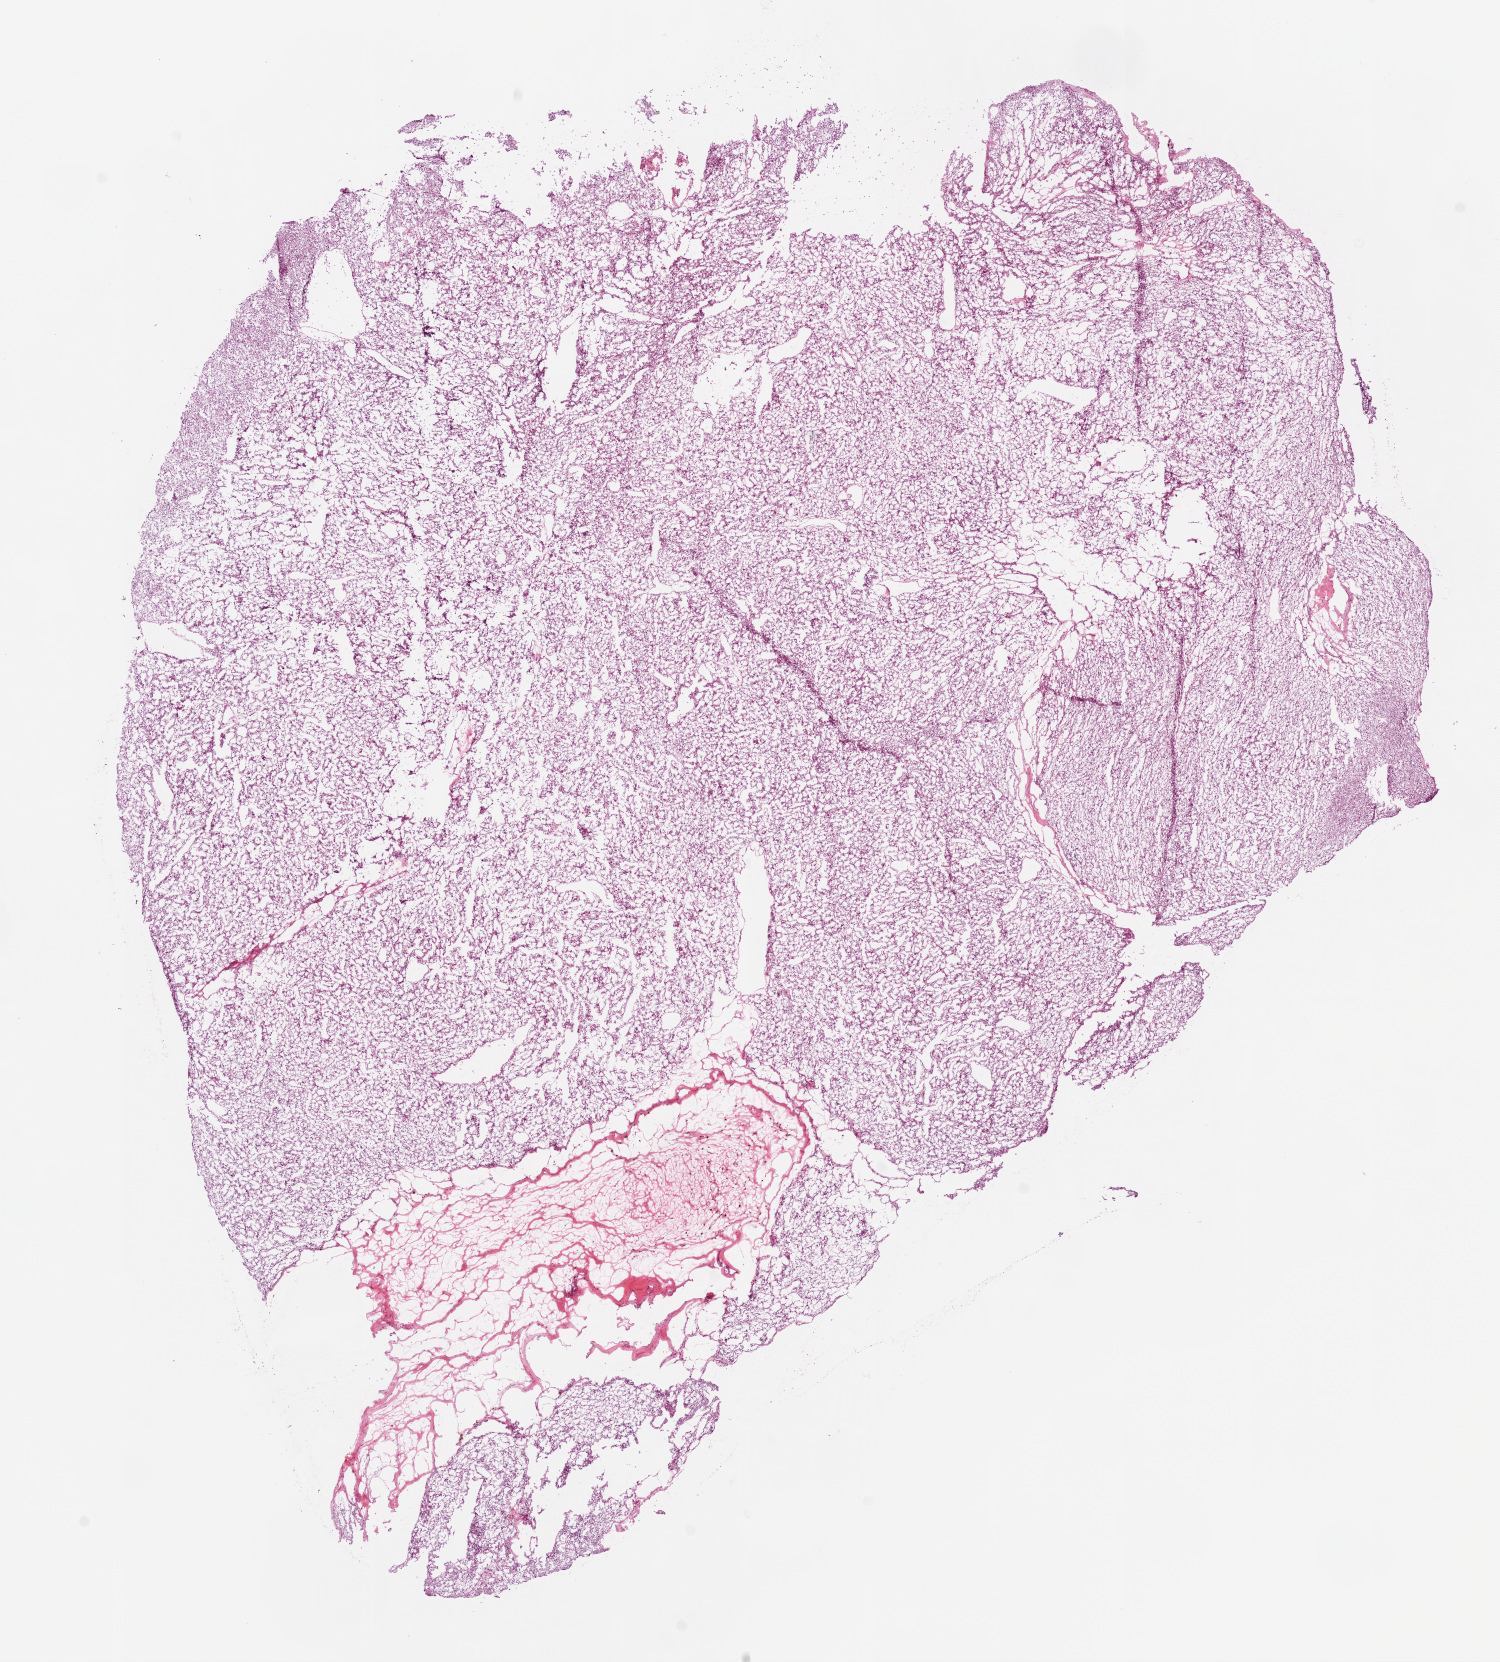
Whole-slide histology image, H&E, whole scanned area (about 12.0 x 13.3 mm, from a 20x scan) shown as a low-resolution overview; frozen section from the bottom of the tissue portion; kidney, primary tumour sample. Patient: male, age at initial diagnosis 56 years. Histologic grade: G2 (moderately differentiated). Composition of this section per pathologist review: tumour cells 90%, tumour nuclei 85%, normal cells 0%, stromal cells 10%, necrosis 0%.
* AJCC pathologic stage: I (7th edition)
* histologic diagnosis: Clear cell adenocarcinoma, NOS